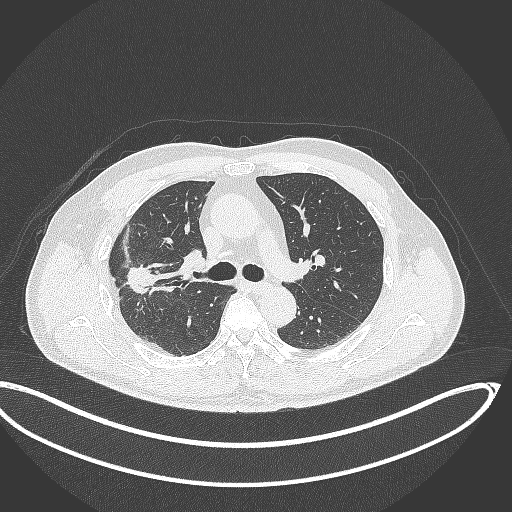
Chest CT, one axial slice. Slice 220 of 391 in the series (ordered by position). 120 kVp. Lung window (W 1500 / L -600 HU). 1 mm slice thickness. 512 × 512 image matrix. Patient: male, 63 years. From the clinical record (not read from this slice): clinical TNM (as recorded): T1c N0 M0; histopathological grade: G2-3.
Annotated regions visible in this slice (rectangle marked by the reading radiologist):
- lung tumour (recorded histology: adenocarcinoma): bounding box <119,257,158,301> (left, top, right, bottom; pixels)